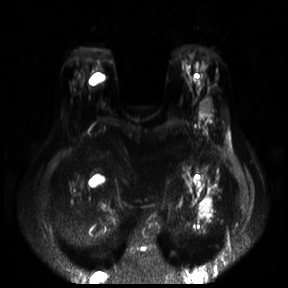
Breast MRI, one axial slice; position 8 of 30 along the scan axis; diffusion-weighted series; image 2 of 4 stored at this slice position (different b-values; order by instance number); 3 T; 288 × 288 image matrix, field of view 360 × 360 mm. Female patient.
Annotated regions visible in this slice (manually delineated by an expert):
- tumour on diffusion-weighted imaging: bounding box [x1, y1, x2, y2] px = [199, 96, 212, 115]